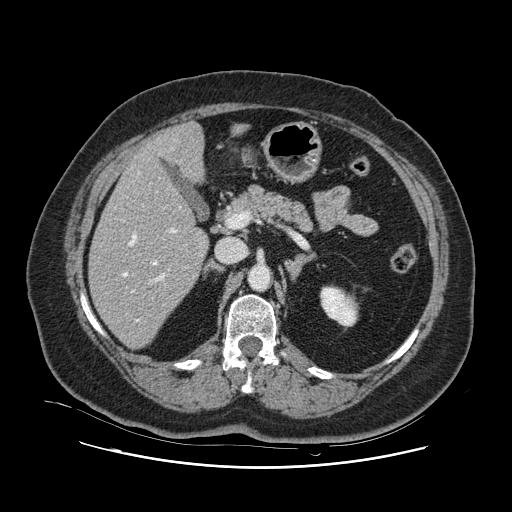
Contrast-enhanced abdominal CT, one axial slice. Position 56 of 132 along the scan axis. Intravenous contrast given. Soft-tissue window (W 400 / L 40 HU). 2.5 mm slice thickness. 512 × 512 image matrix, field of view 391 × 391 mm. Female patient, age 73 years. From the clinical record (not read from this slice): diagnosis: colorectal cancer liver metastases, imaged before liver resection; multiple liver metastases: no; largest metastasis: 7 cm; chemotherapy before resection: yes.
Annotated regions visible in this slice (expert manual segmentation):
- hepatic veins: bounding box (x1, y1, x2, y2) in pixels: (123, 148, 181, 322)
- liver: (90, 124, 208, 348)
- planned liver remnant (the part of the liver to remain after resection): (90, 148, 208, 348)
- portal vein (with intrahepatic branches): (131, 228, 177, 292)